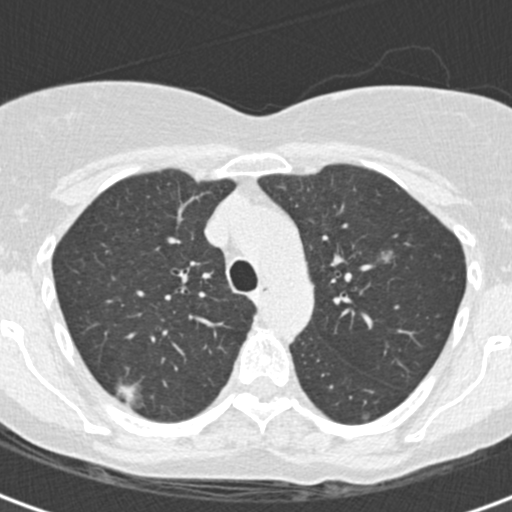
Low-dose screening chest CT, one axial slice. Position 127 of 172 along the scan axis. Reconstruction kernel B30f. Lung window (W 1500 / L -600 HU). 2 mm slice thickness. 512 × 512 image matrix, field of view 283 × 283 mm.
Outlined on this slice (outlined manually by an expert reader):
- lesion 1 (tumor, upper lobe of right lung): bounding box <115,381,145,408> (left, top, right, bottom; pixels)